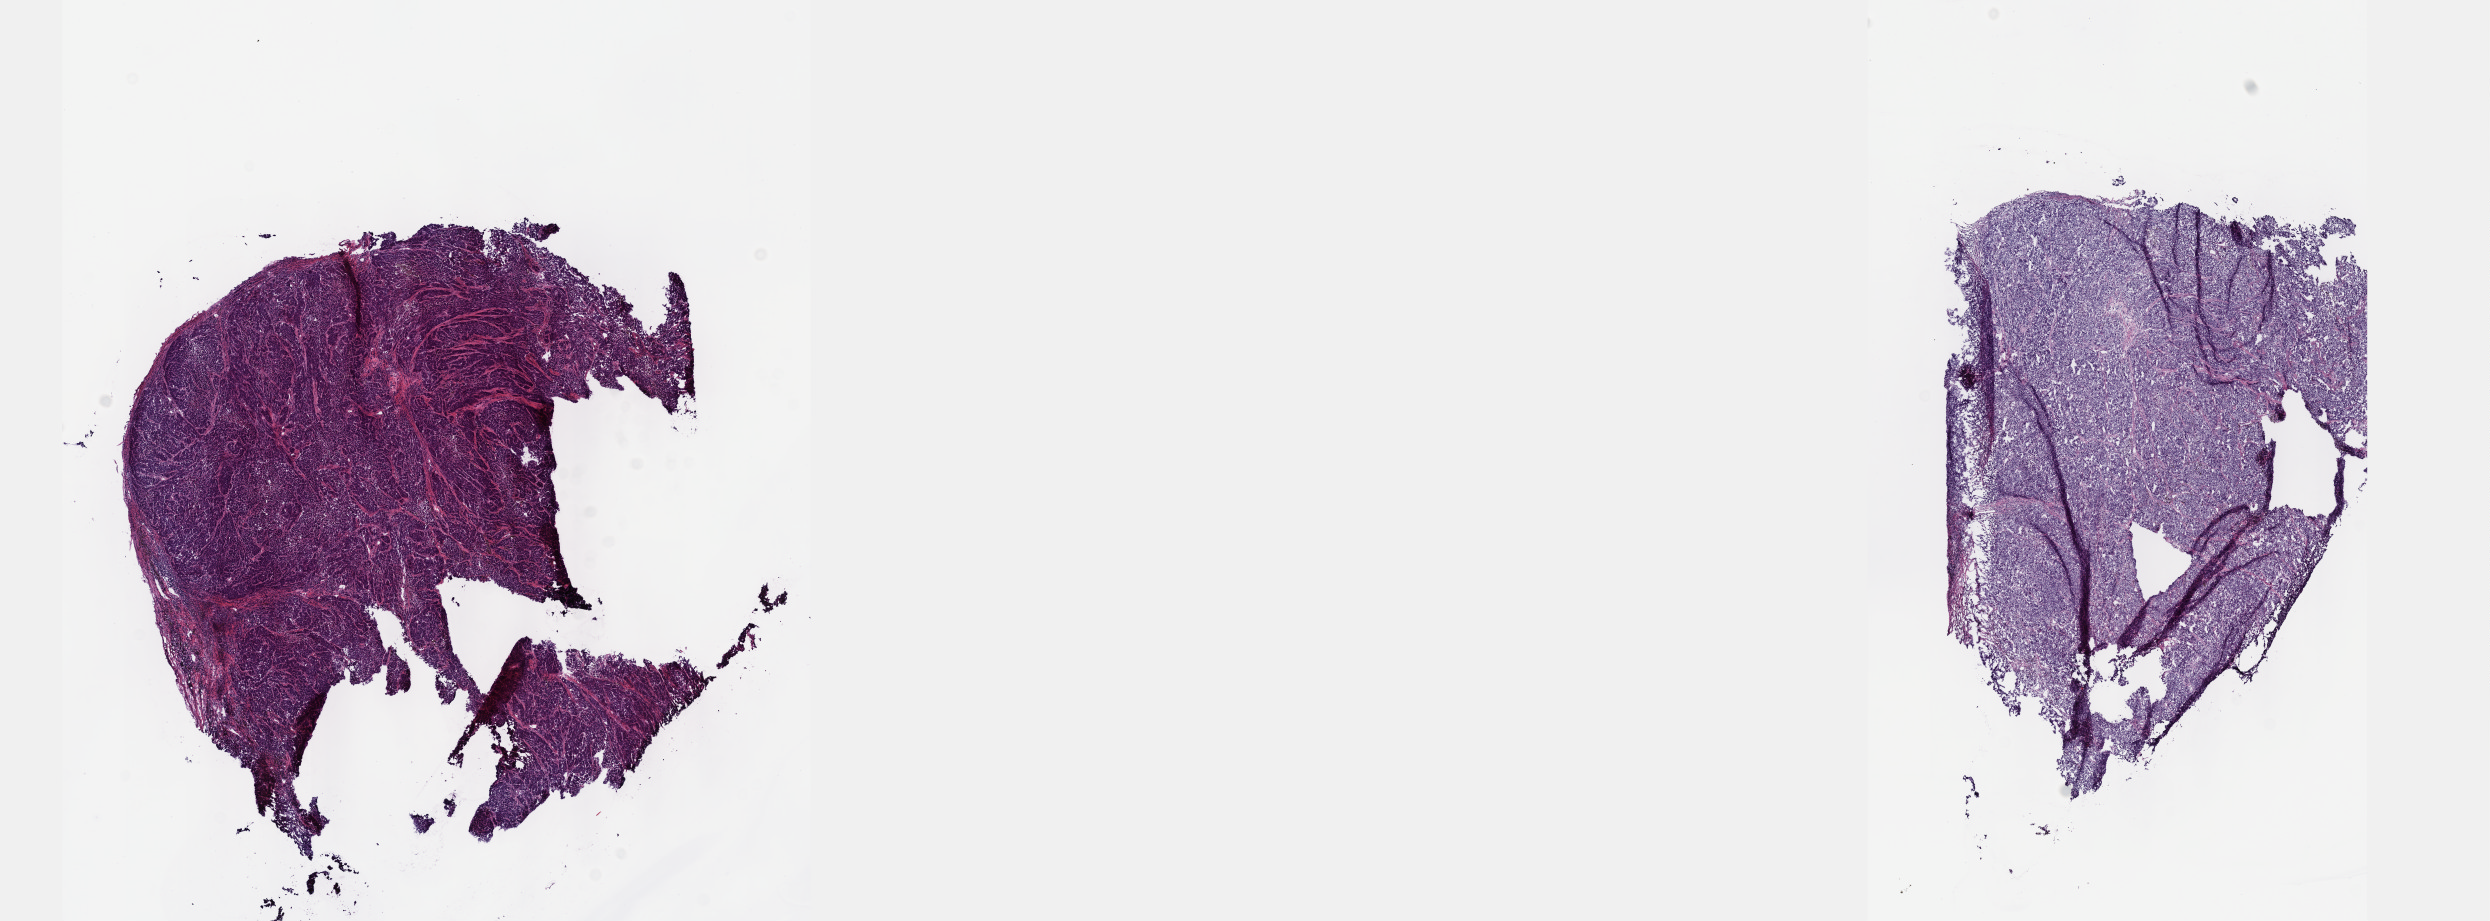
Digitized H&E tissue section (whole slide), low-resolution overview of the scanned area, about 20.1 x 7.4 mm. Frozen section from the top of the tissue portion. Primary tumour sample from the skin. Male patient; age at initial diagnosis 66 years. Pathologist review of this section (percent, as recorded): tumour cells 85%, tumour nuclei 90%, normal cells 0%, stromal cells 10%, necrosis 5%. Infiltration values recorded for this section: lymphocyte infiltration 0%, monocyte infiltration 0%, neutrophil infiltration 0%.
* AJCC pathologic stage: IIC
* diagnosis: Malignant melanoma, NOS